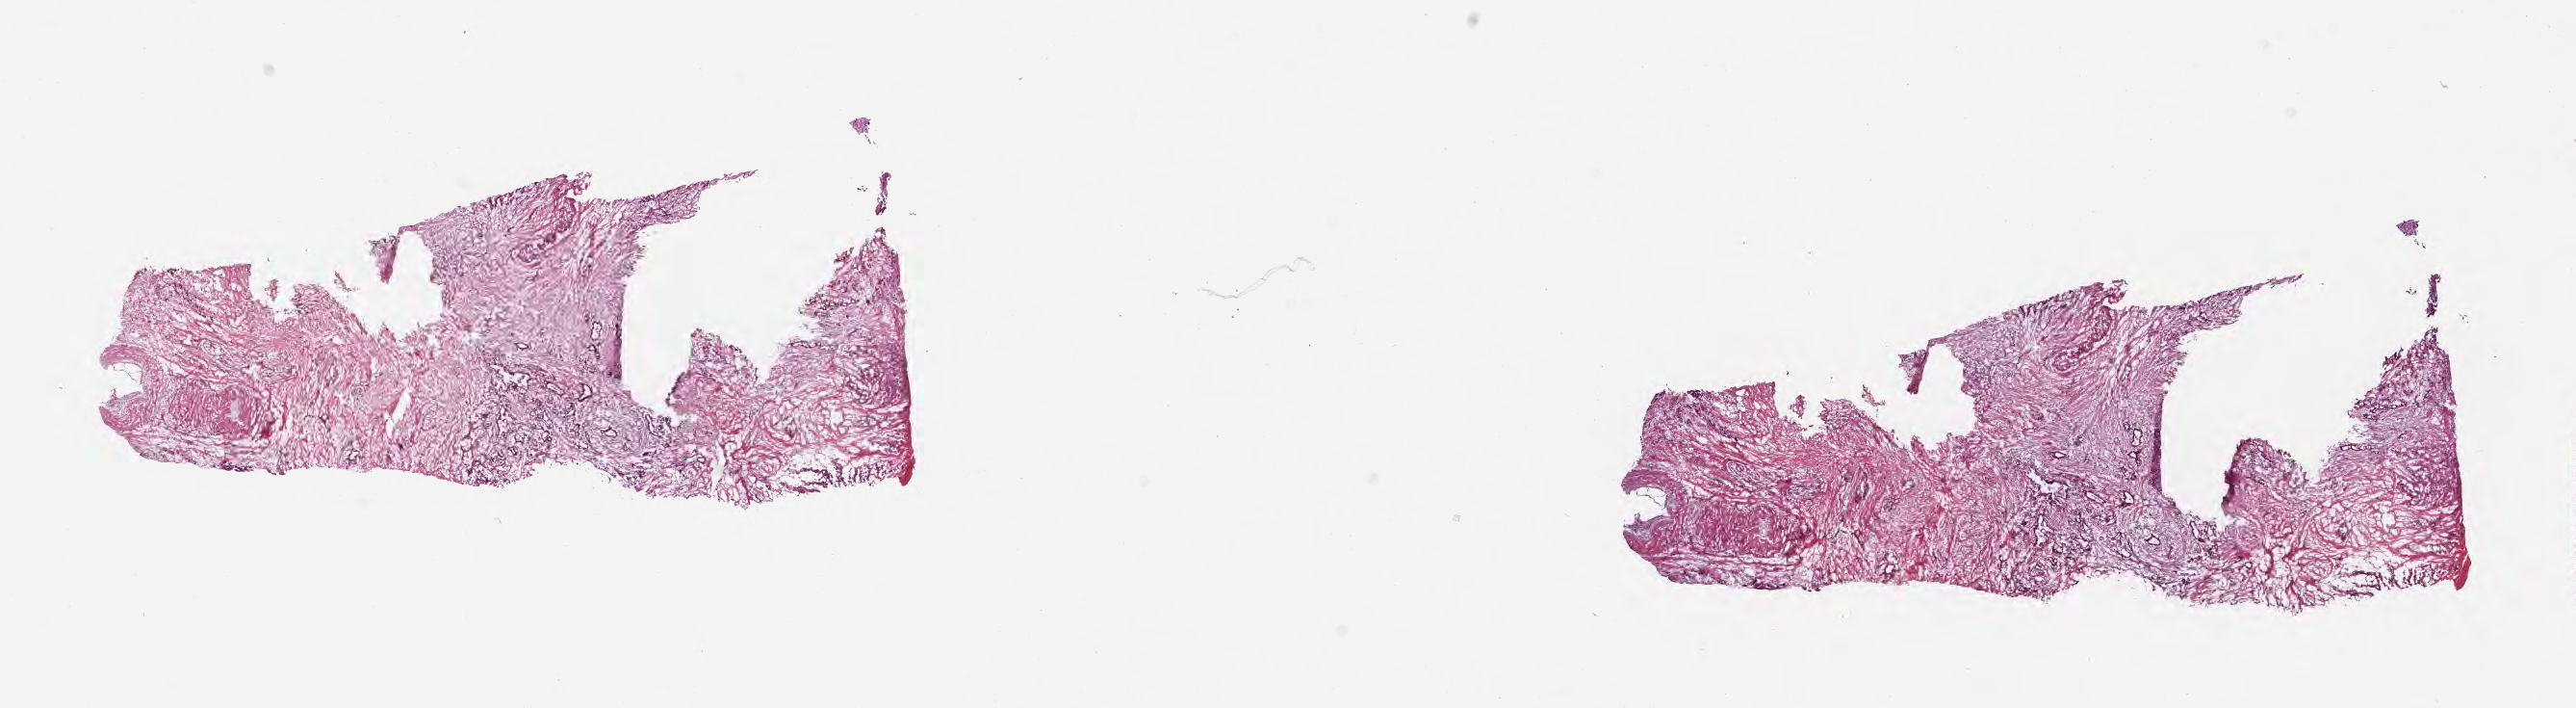
Whole-slide image, hematoxylin and eosin (H&E) stain — low-resolution overview of the scanned area, about 21.6 x 5.9 mm, frozen section (tissue freezing medium), primary tumor, site: head of pancreas. Female patient; age at initial diagnosis 61 years. Pathologist review of this section (percent, as recorded): tumor cells 65%, tumor nuclei 65%.
Diagnosis: Infiltrating duct carcinoma, NOS.